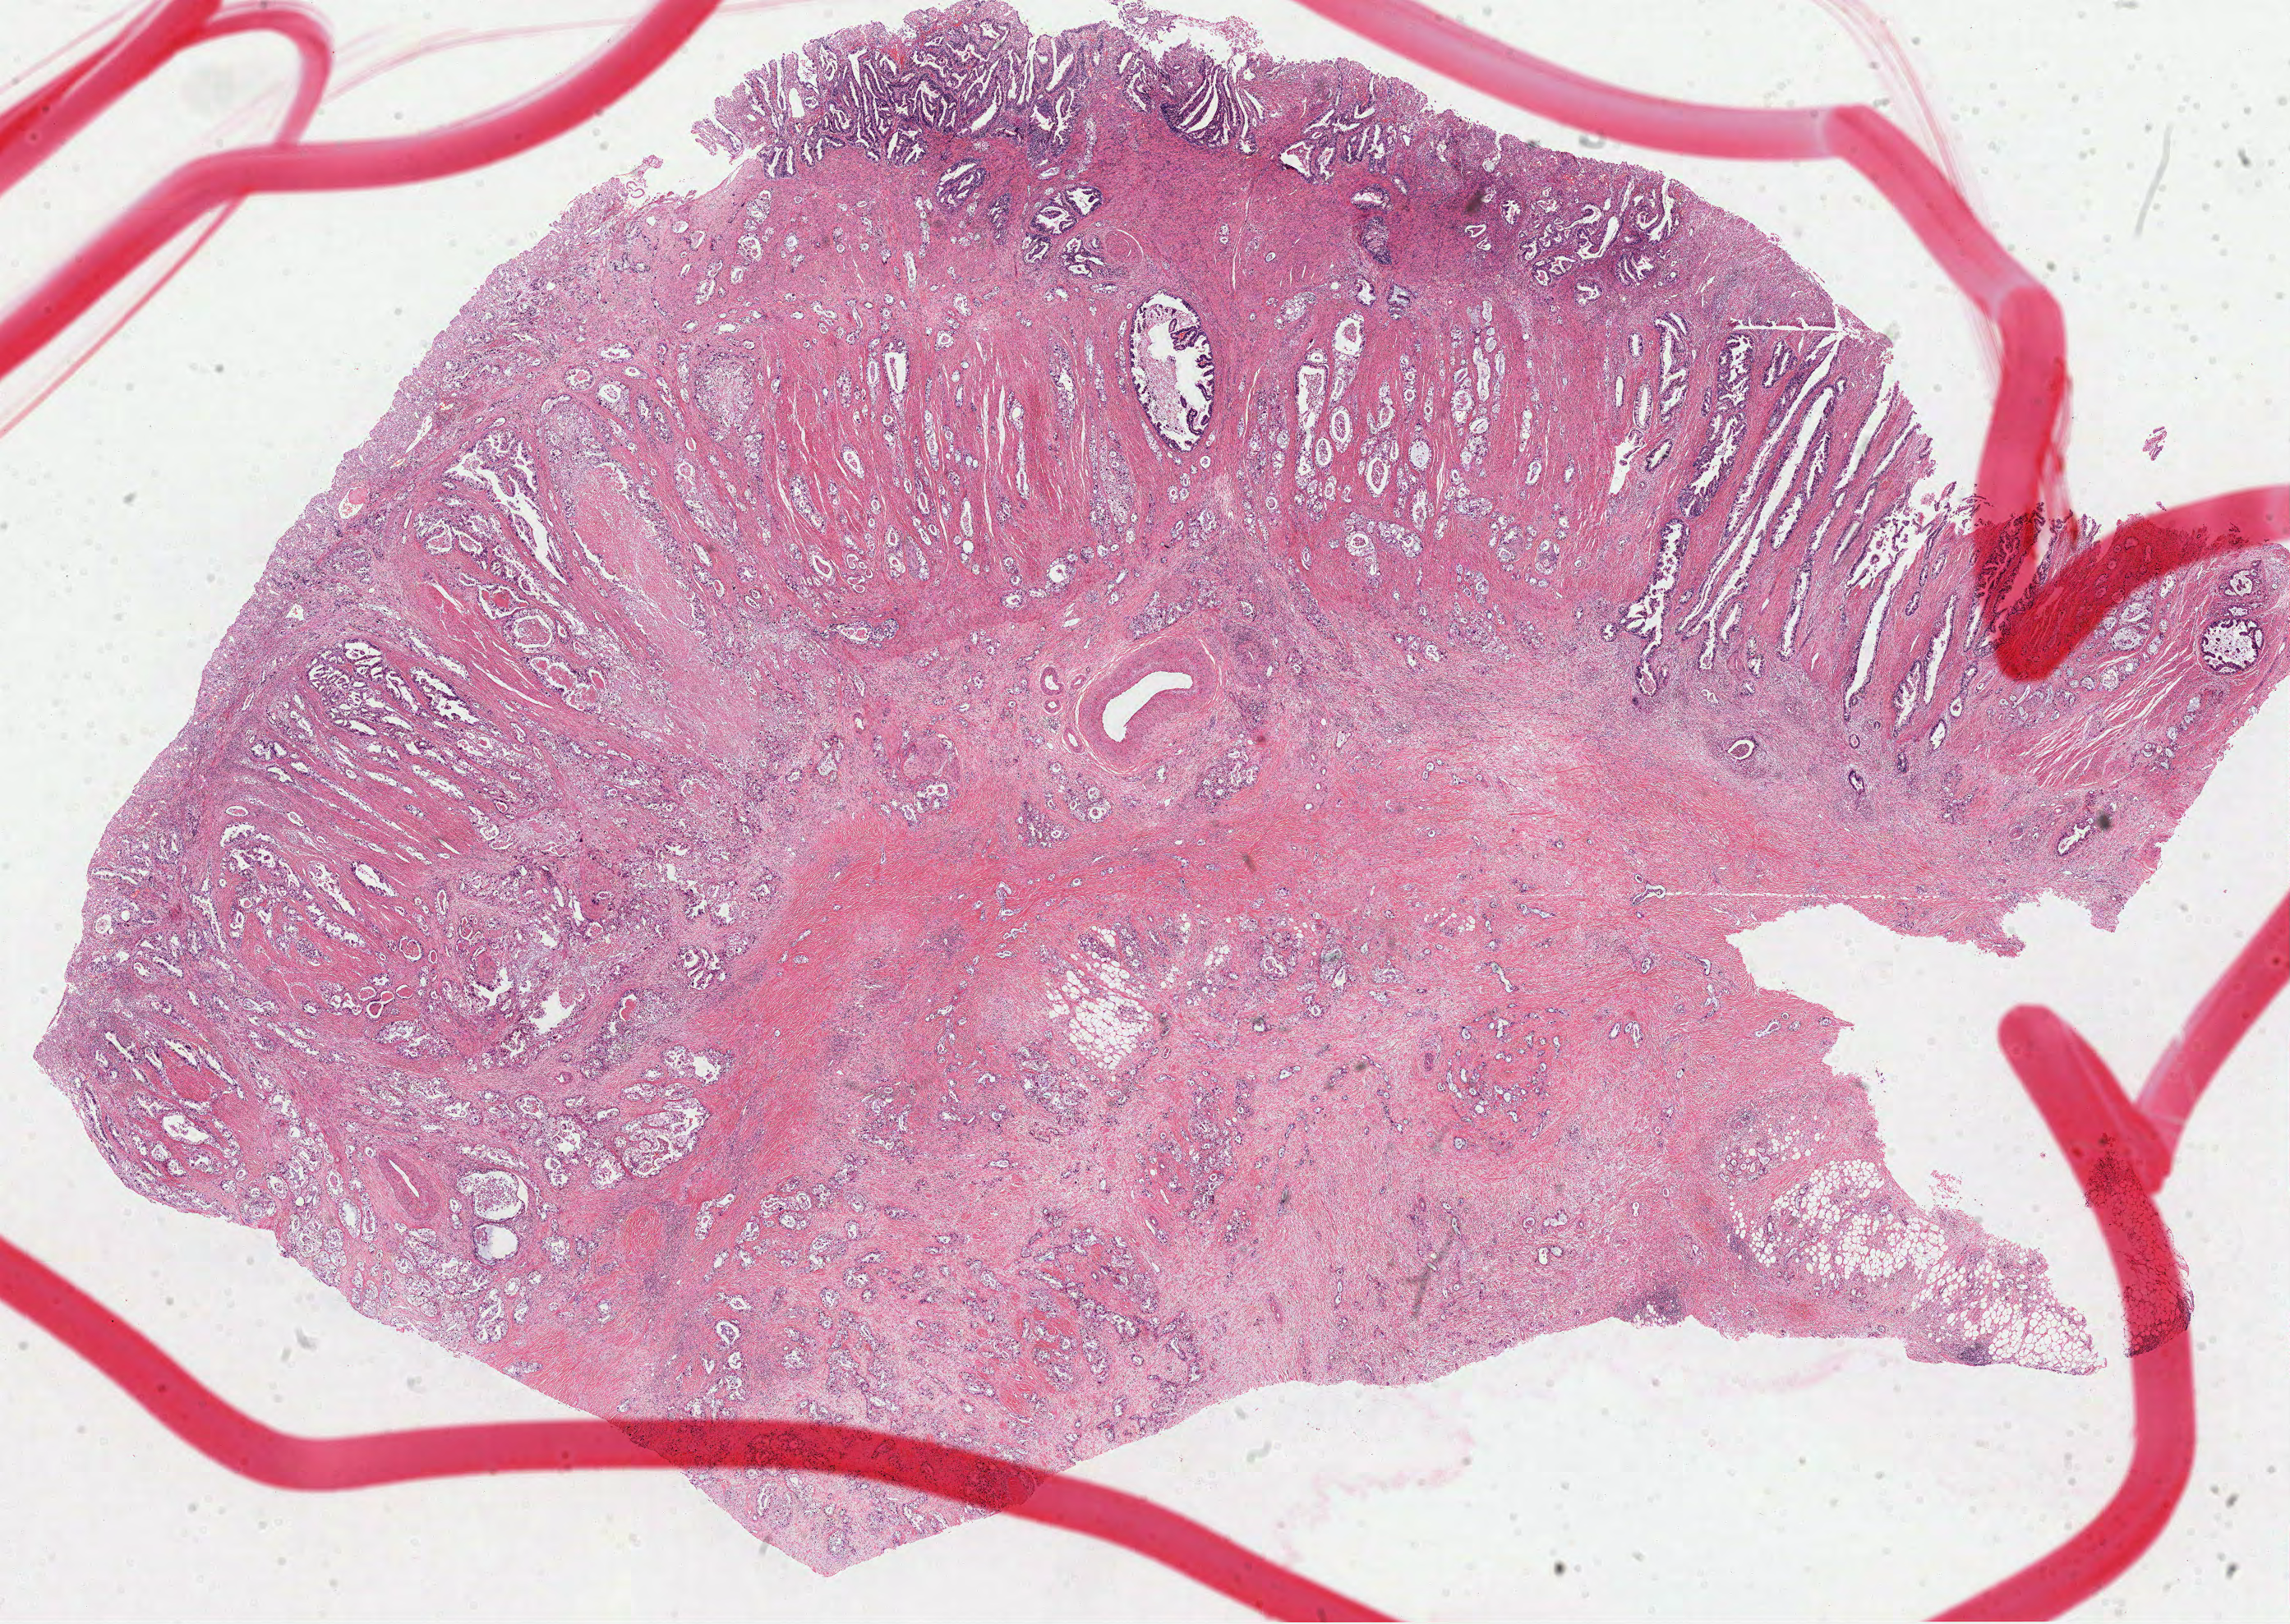
Whole-slide histology image, H&E-stained, whole scanned area (about 22.5 x 15.9 mm, from a 40x scan) shown as a low-resolution overview. Formalin-fixed paraffin-embedded (FFPE) diagnostic section. Stomach, primary tumour sample. Male, age 74 years at initial diagnosis. Histologic grade: G2 (moderately differentiated).
TNM: T3 N1 M0. Histologic diagnosis: Adenocarcinoma, NOS (cardia, NOS). AJCC pathologic stage: IIB (7th edition). Lymph nodes positive (case pathology): 2 of 15 examined.